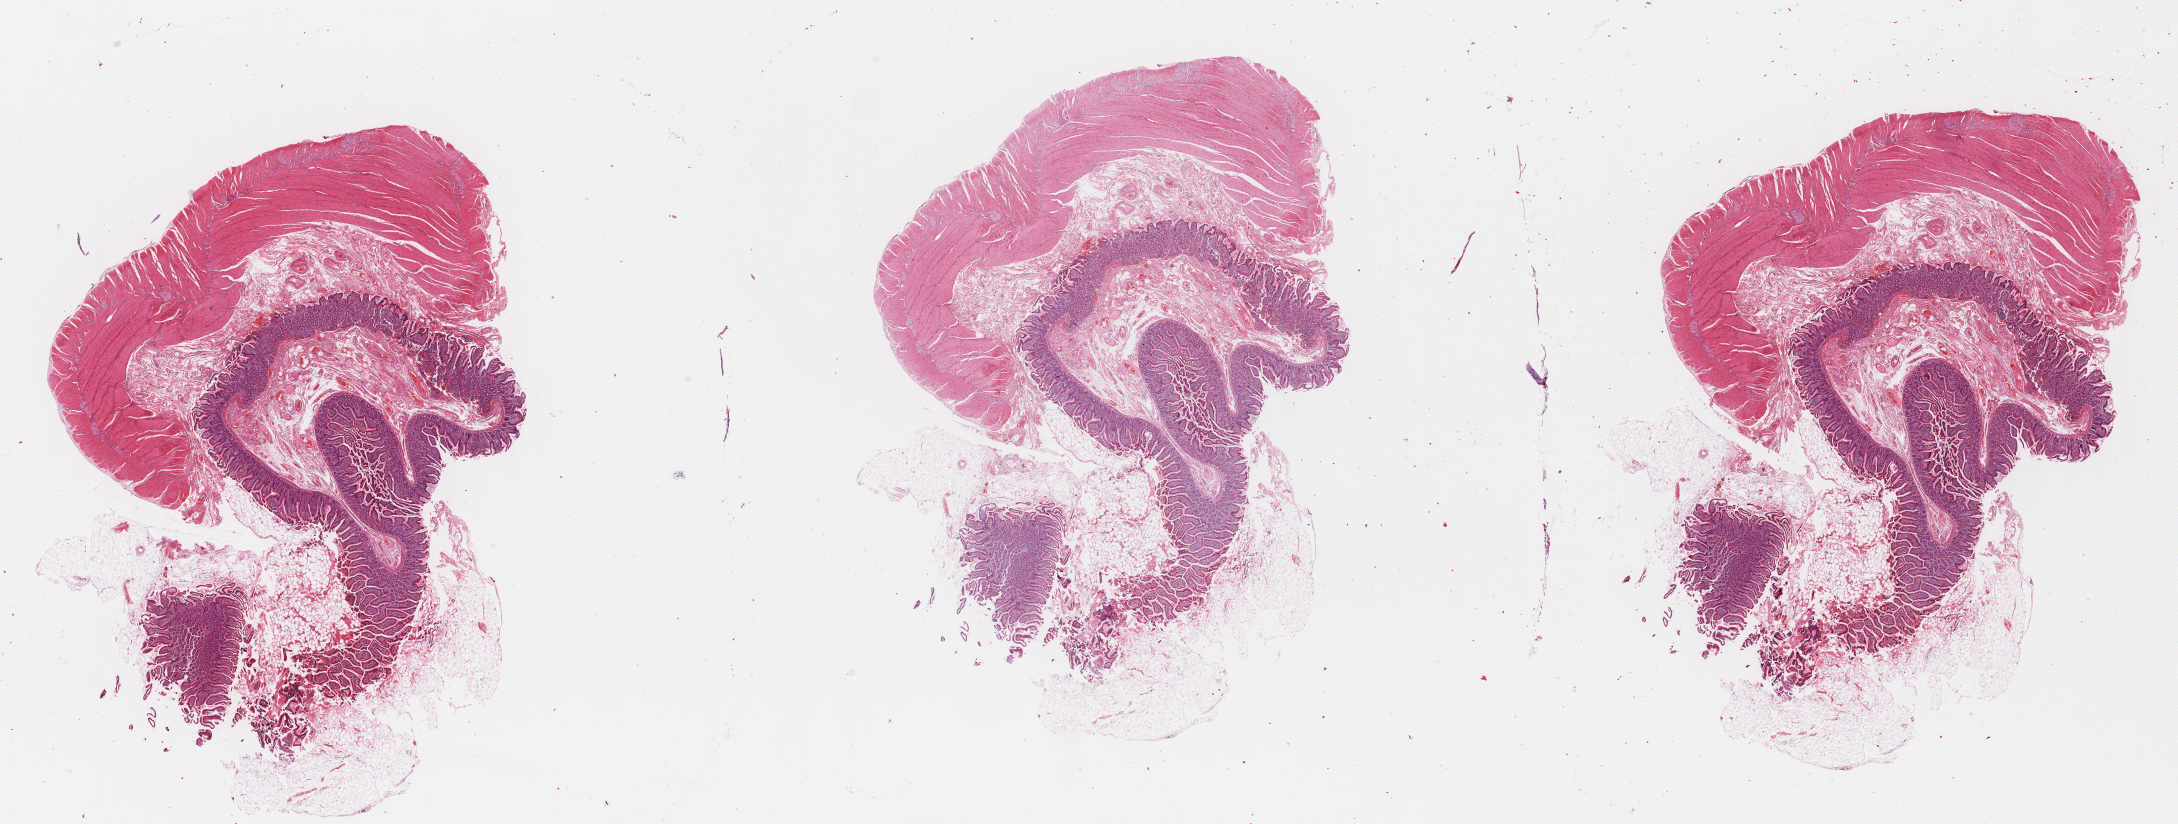
Whole-slide histology image, H&E — whole scanned area (about 35.2 x 13.3 mm, slide scanned at 40x) shown as a low-resolution overview, FFPE section, solid tissue normal (non-tumour tissue) sample from the pancreas. Patient: male, age at initial diagnosis 50 years.
This section: solid tissue normal sample (biorepository sample class). Patient diagnosis: Infiltrating duct carcinoma, NOS (head of pancreas).